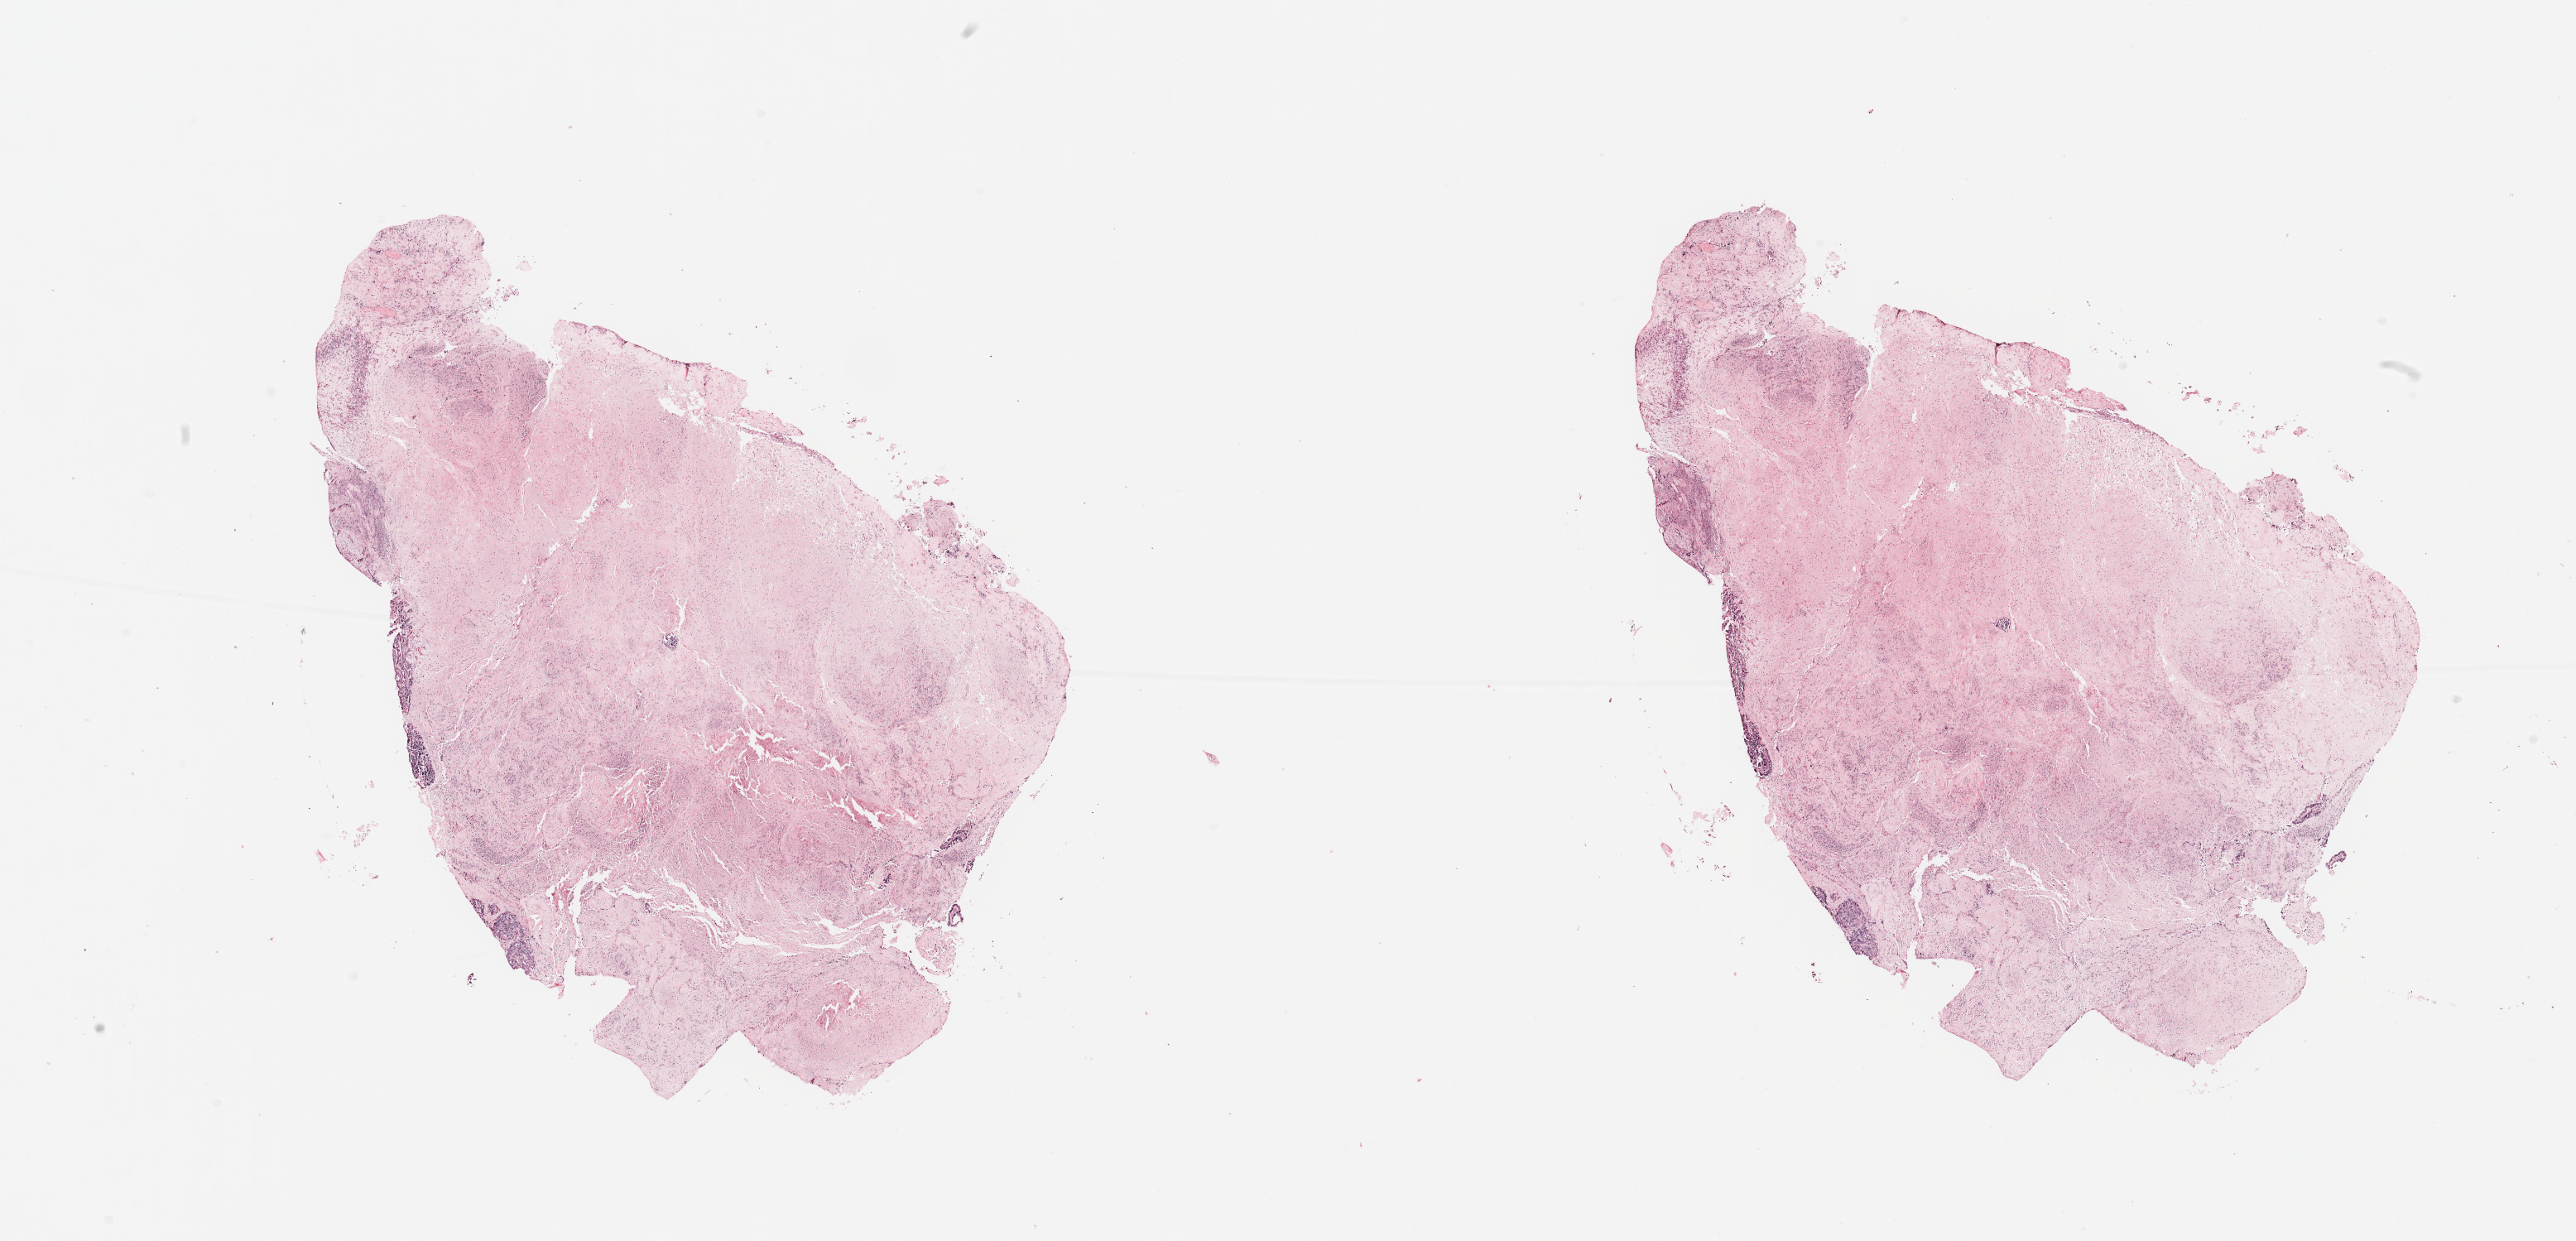
Digitized H&E-stained tissue section (whole slide) — a low-resolution overview of the entire scanned area, about 24.6 x 11.9 mm. Tumour tissue sample, uterus. 81-year-old female patient.
- patient diagnosis (cohort enrolment): corpus endometrial carcinoma (uterus)